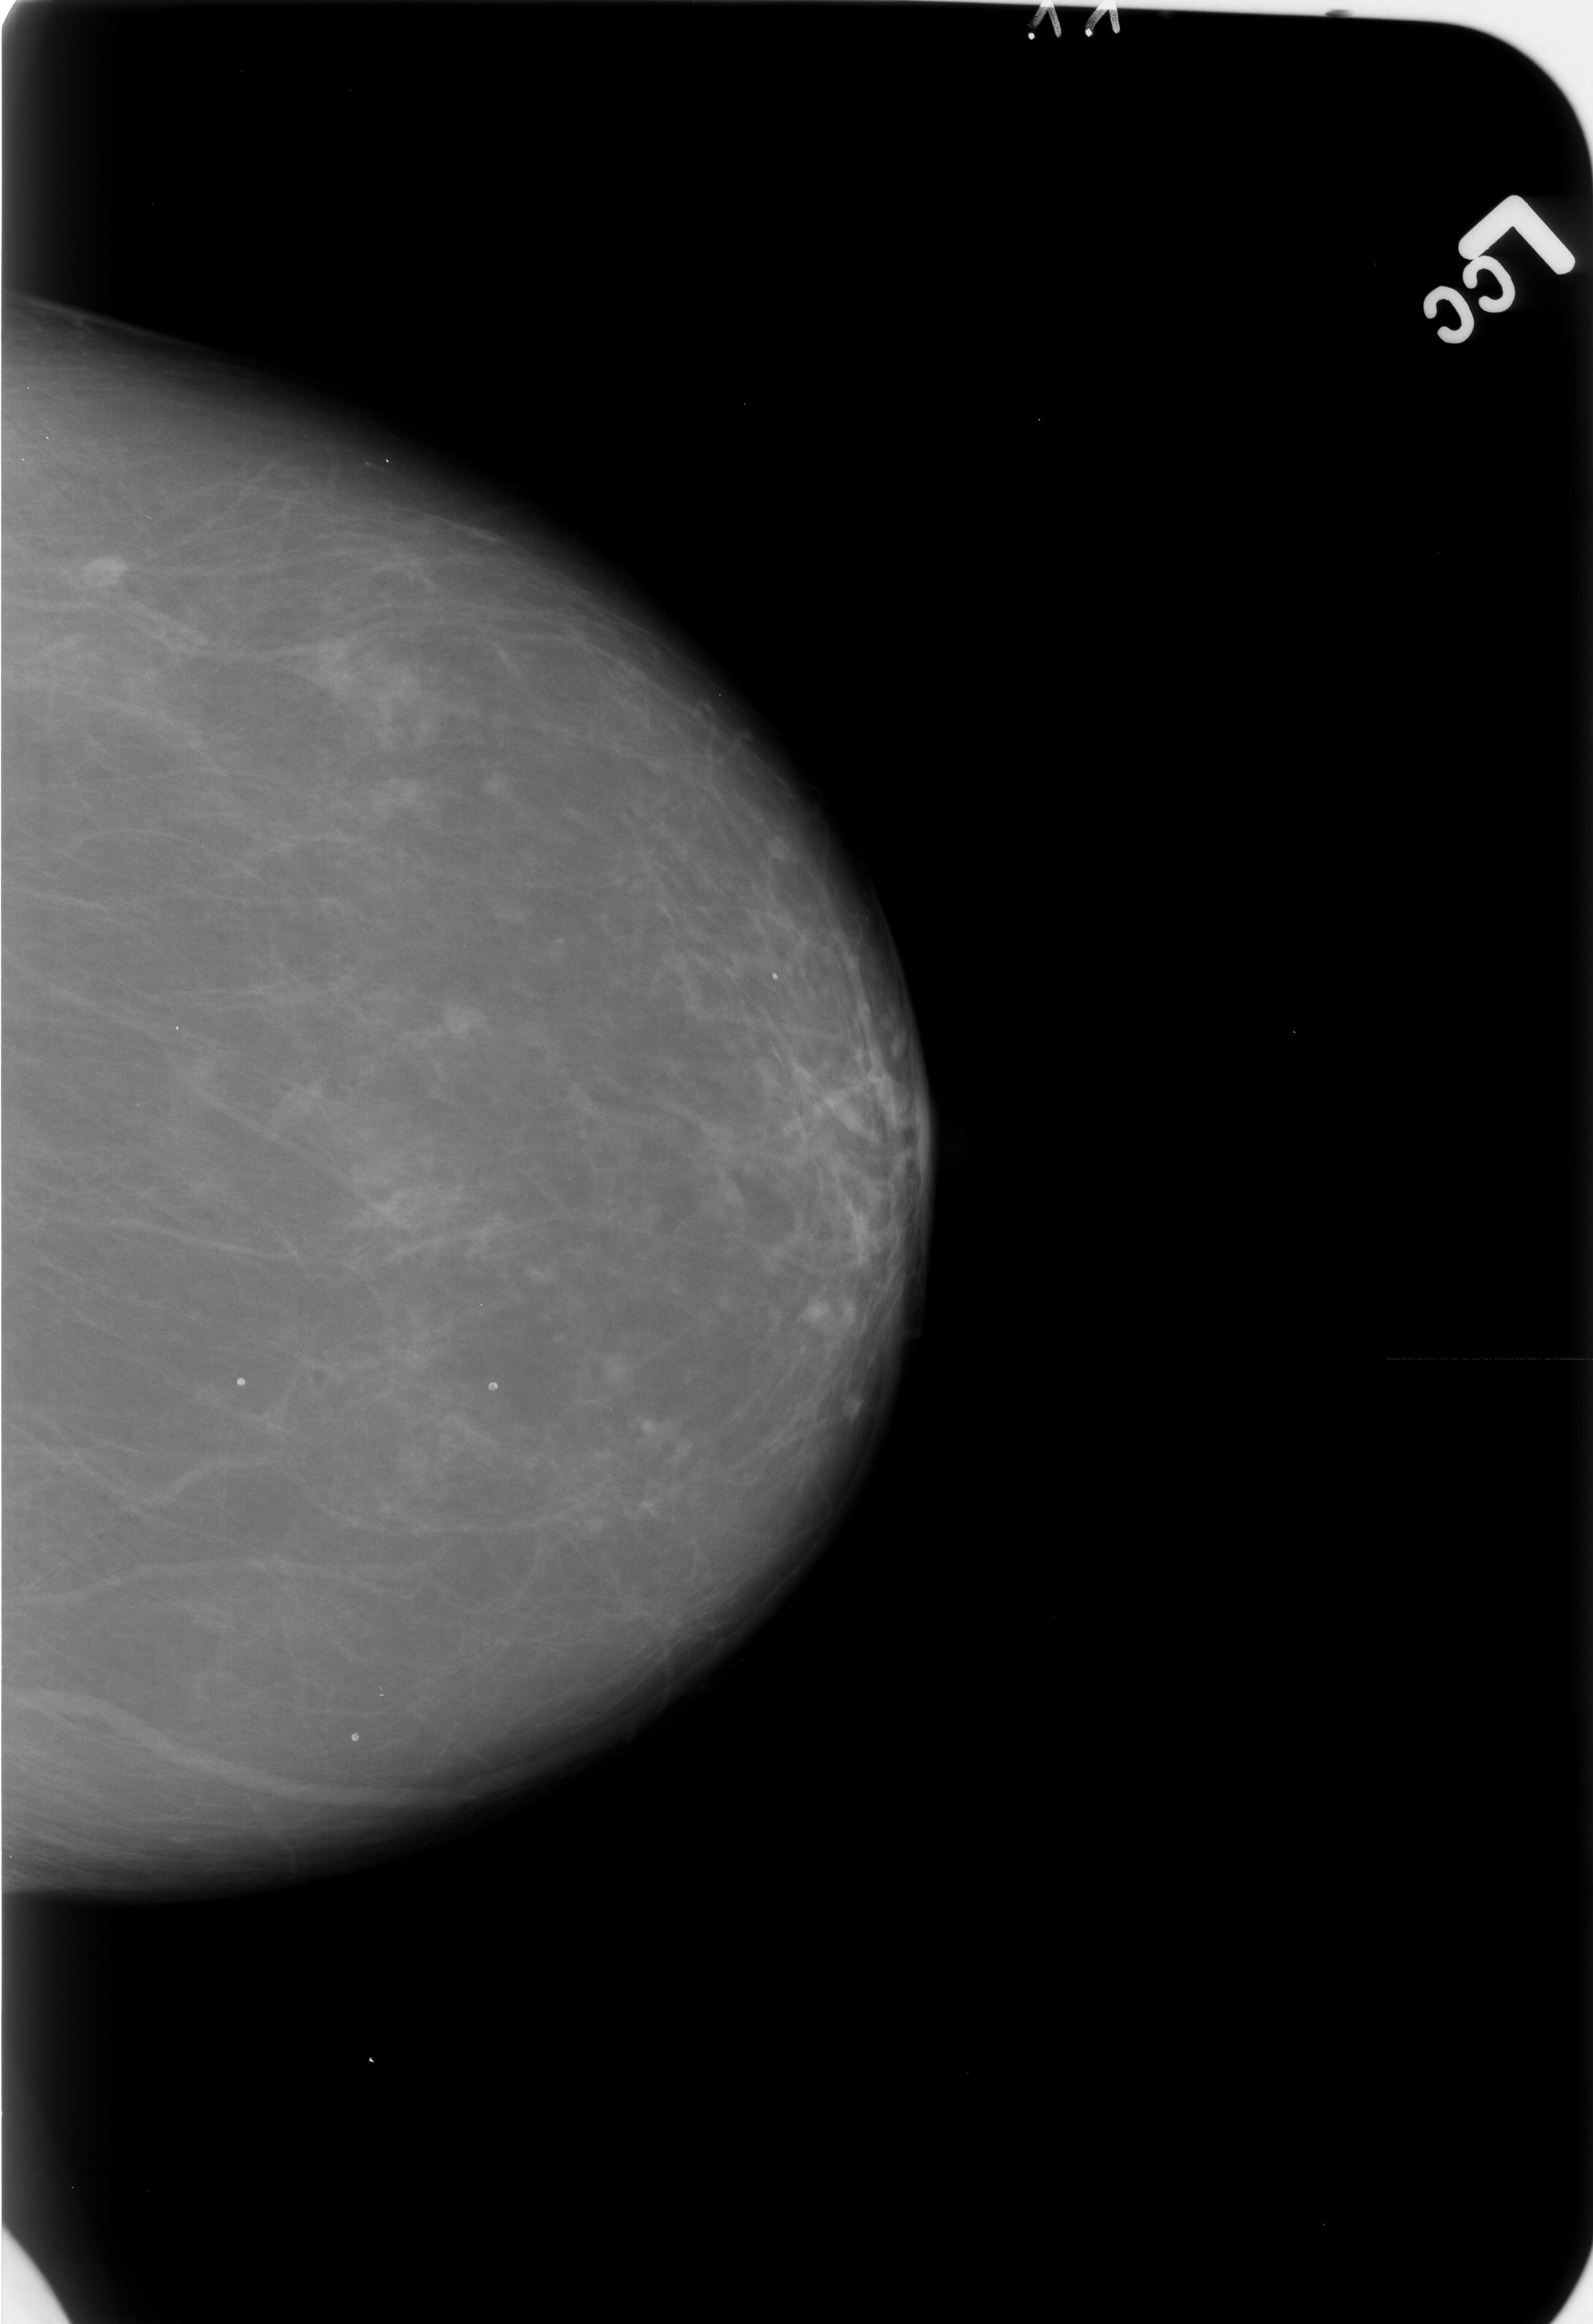
Digitized screen-film mammogram. Left breast. Craniocaudal (CC) view. Breast composition: almost entirely fatty (BI-RADS density category 1 of 4). 1593 × 2324 image matrix.
Expert-marked regions of interest on this film, with their recorded descriptors:
- Finding 1 of 4: calcifications, morphology lucent centered; BI-RADS assessment category 2; benign; no additional work-up was recommended (outcome (as recorded, no biopsy): benign without callback): bounding box <226,1366,253,1401> (left, top, right, bottom; pixels)
- Finding 2 of 4: calcifications, morphology lucent centered; BI-RADS assessment category 2; outcome (as recorded, no biopsy): benign without callback (not worked up further): <340,1711,375,1761>
- Finding 3 of 4: calcifications, morphology lucent centered; BI-RADS assessment category 2; subtlety rating 3 on a 1 (subtle) to 5 (obvious) scale; benign; no additional work-up was recommended (outcome (as recorded, no biopsy): benign without callback): <478,1363,512,1410>
- Finding 4 of 4: calcifications, morphology lucent centered; BI-RADS assessment category 2; subtlety rating 3 on a 1 (subtle) to 5 (obvious) scale; benign; no additional work-up was recommended (outcome (as recorded, no biopsy): benign without callback): <753,957,791,994>